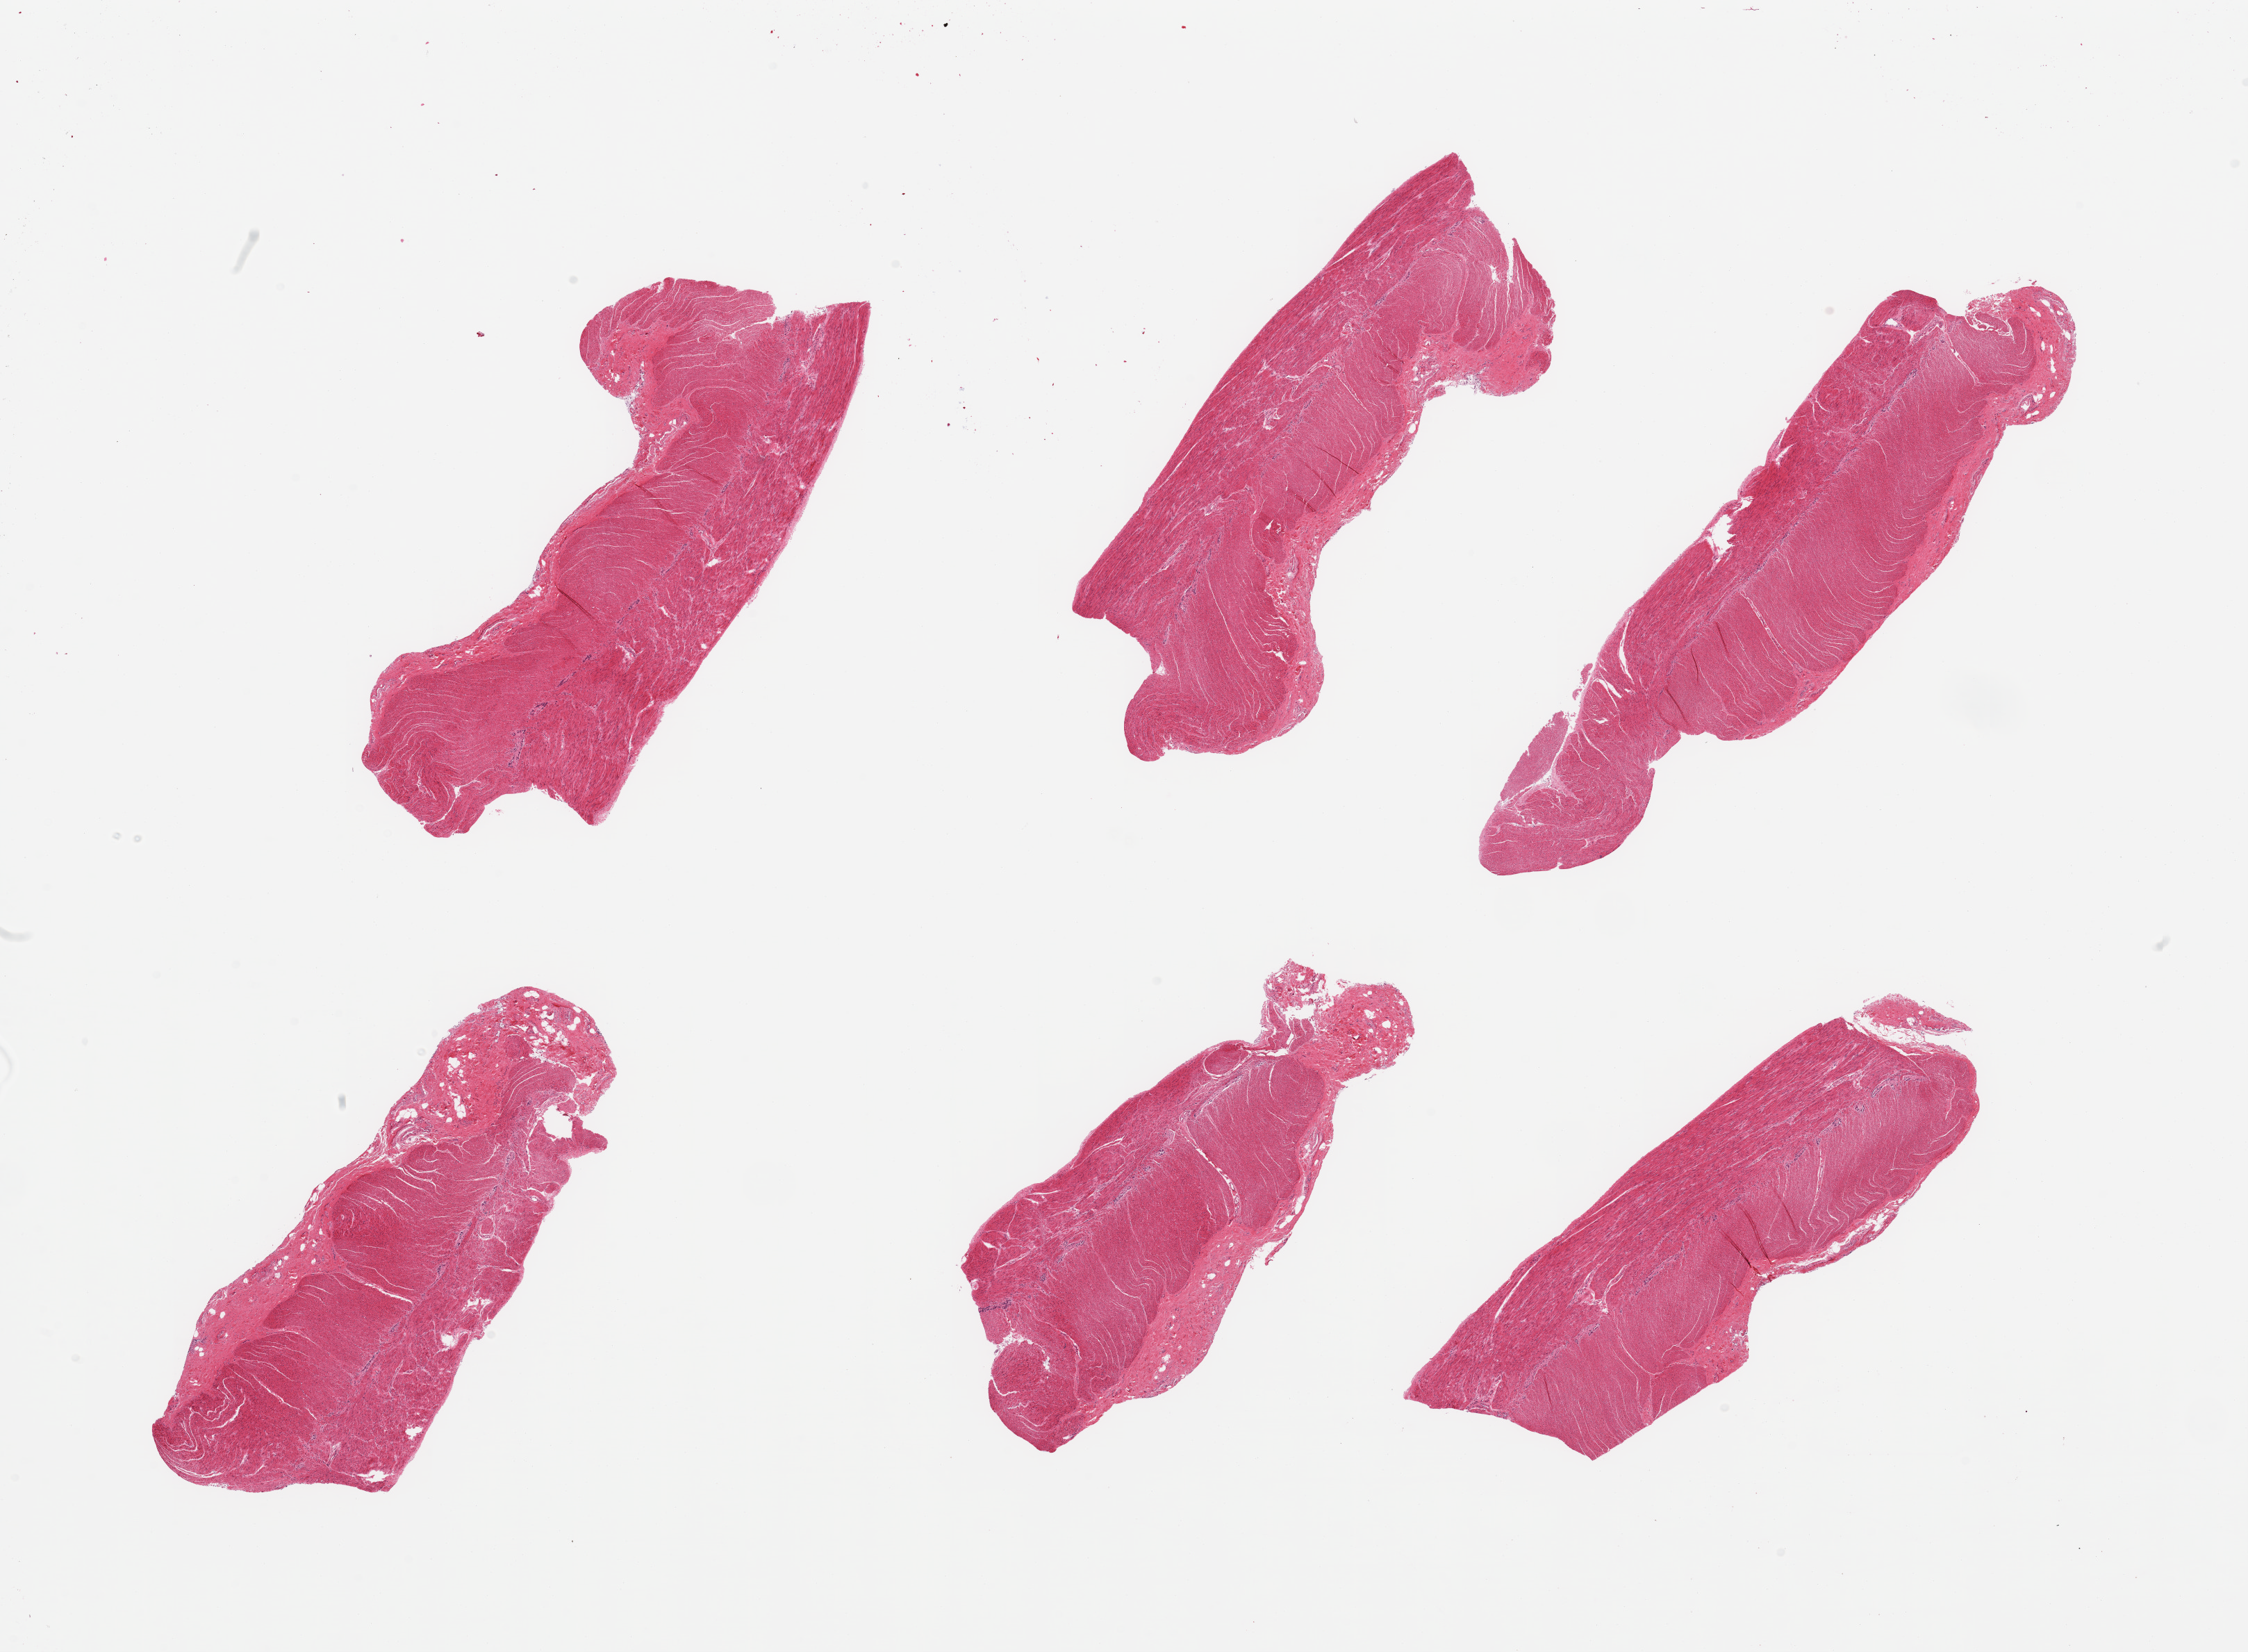
Whole-slide image, haematoxylin and eosin stain, shown as a low-resolution overview of the whole scanned area (about 25.6 x 18.8 mm), PAXgene-fixed, paraffin-embedded tissue, section of sigmoid colon (target tissue), donor tissue sample. Male donor.
Review note (as recorded): 6 pieces, confirmed target muscularis.